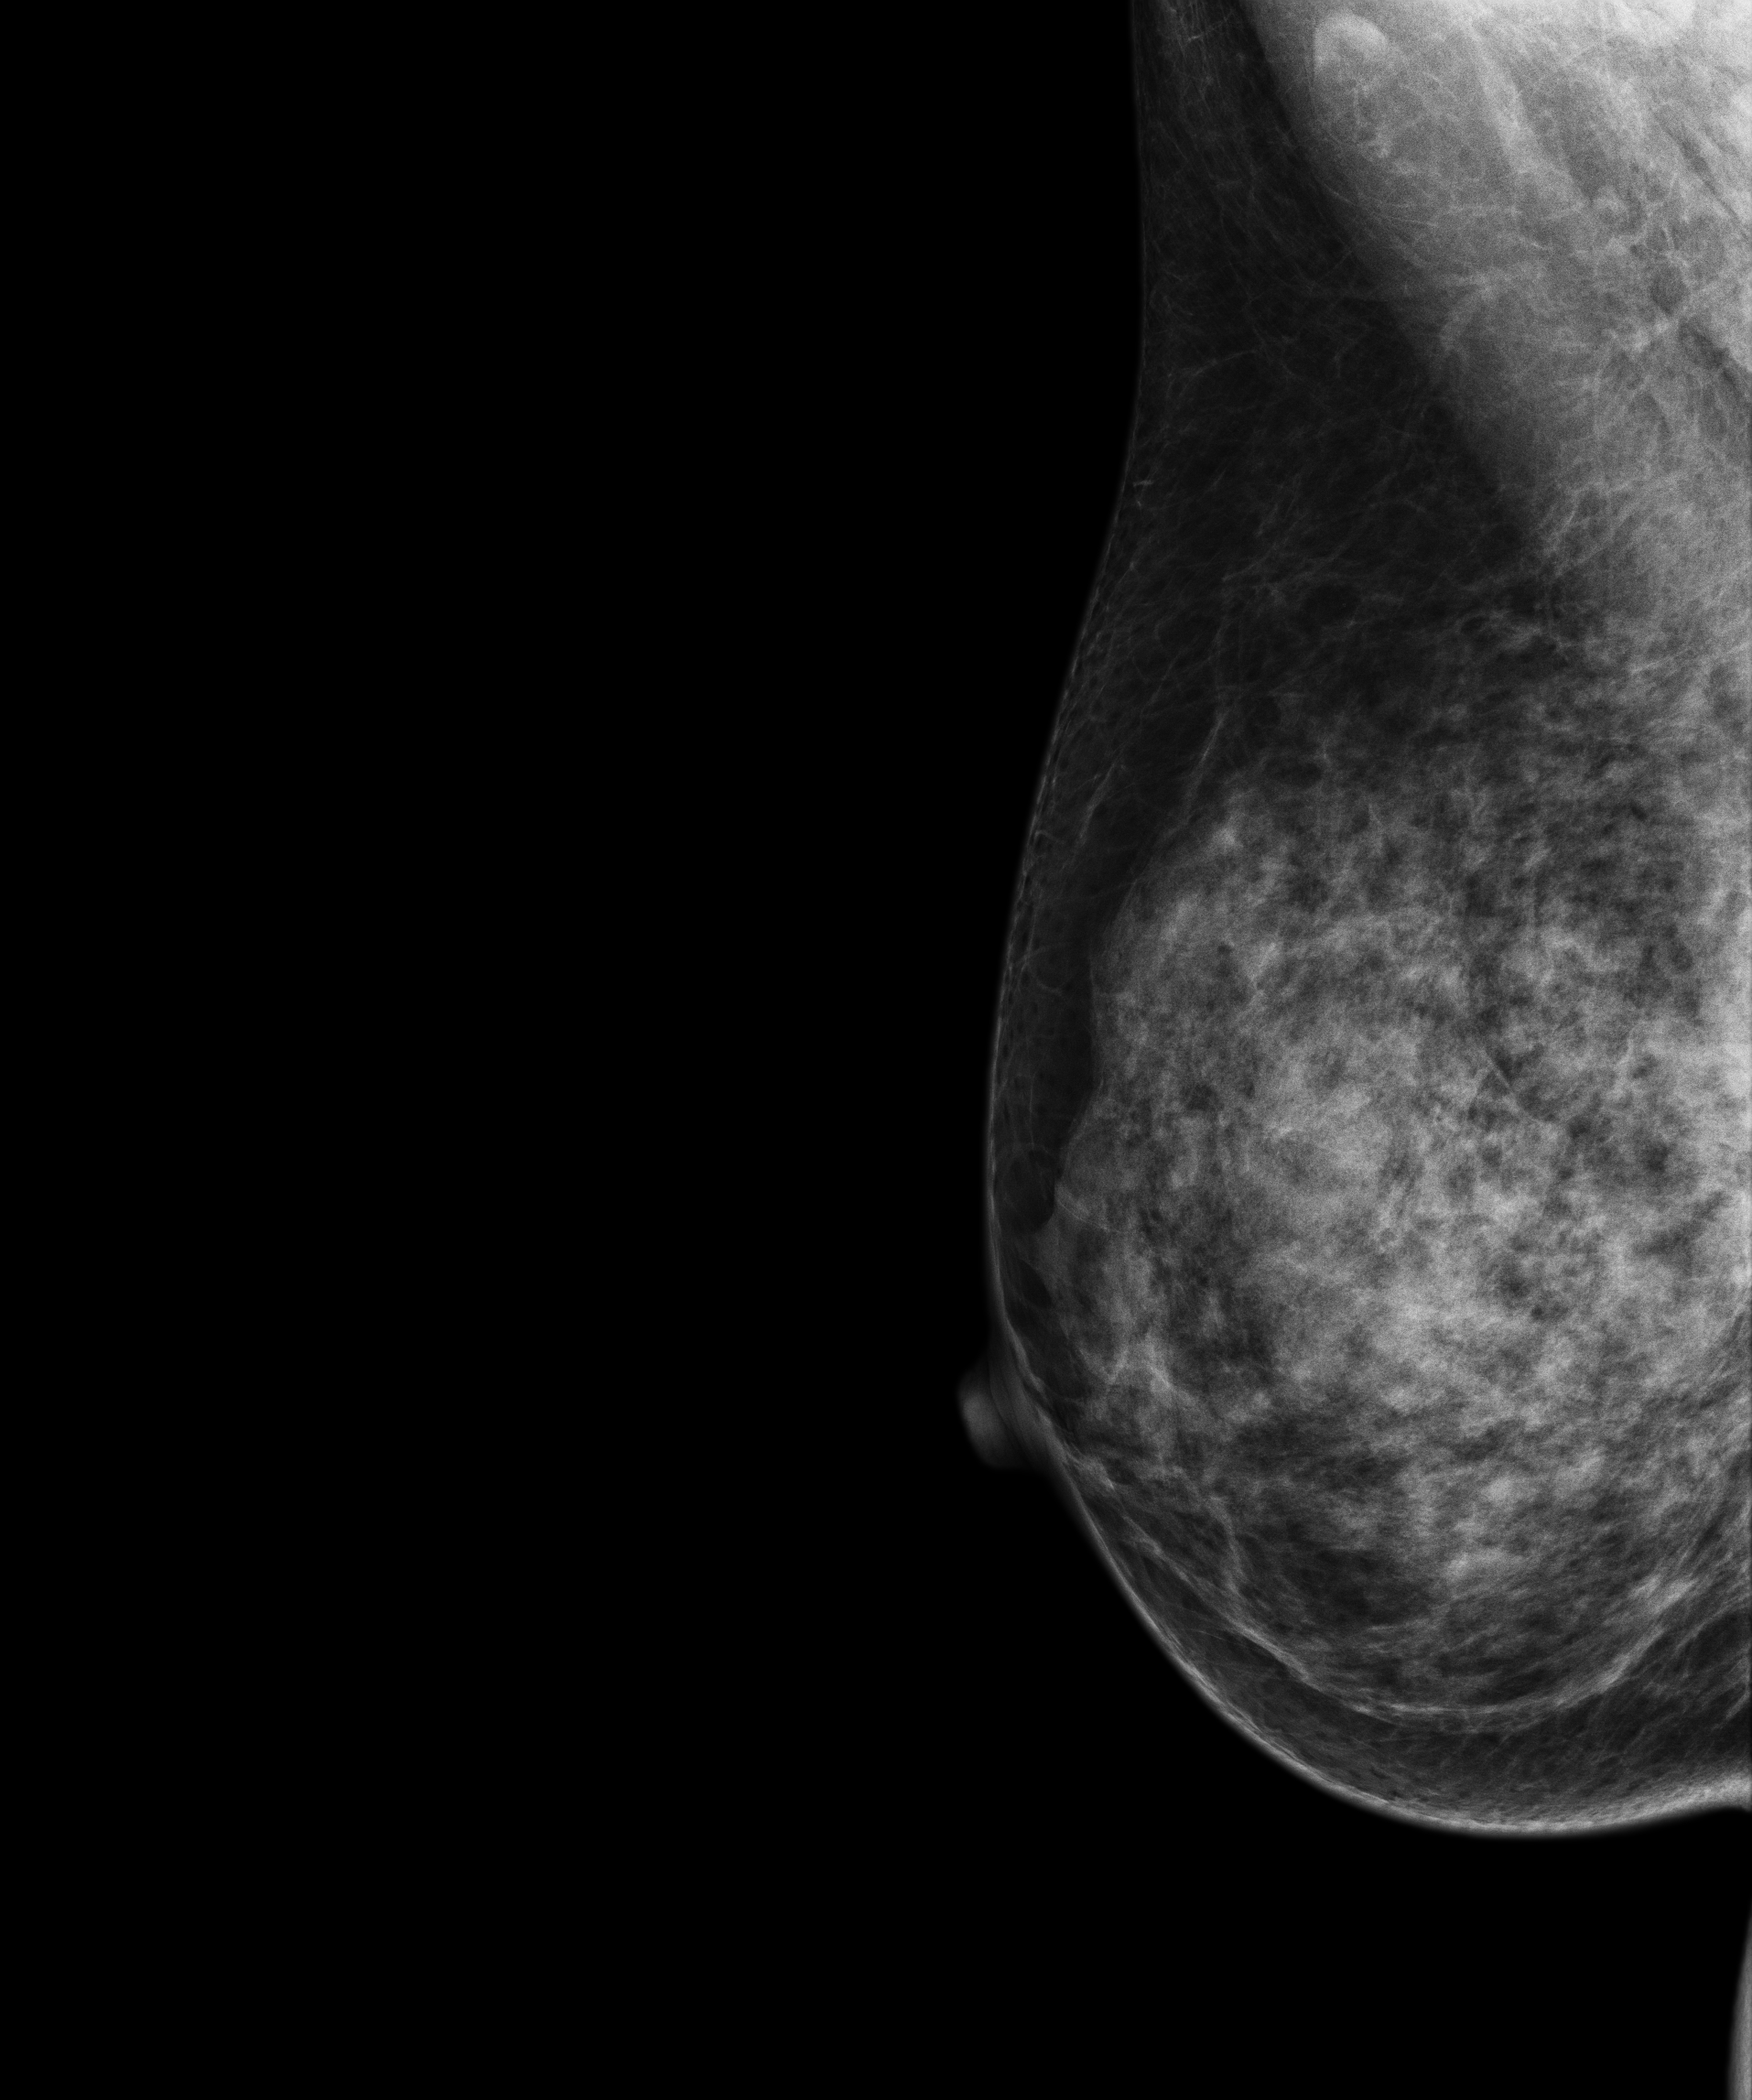
Full-field digital mammogram (FFDM), right breast, mediolateral oblique (MLO) view, screening examination, system: Senographe Essential ADS_56.21.3. Patient aged 60 years (female).
BI-RADS breast density category at the screening exam (both breasts, scale 1–4): 4. Final BI-RADS category for the screening round (tomosynthesis exam, both breasts): category 1. Recall: no recall after this screen.